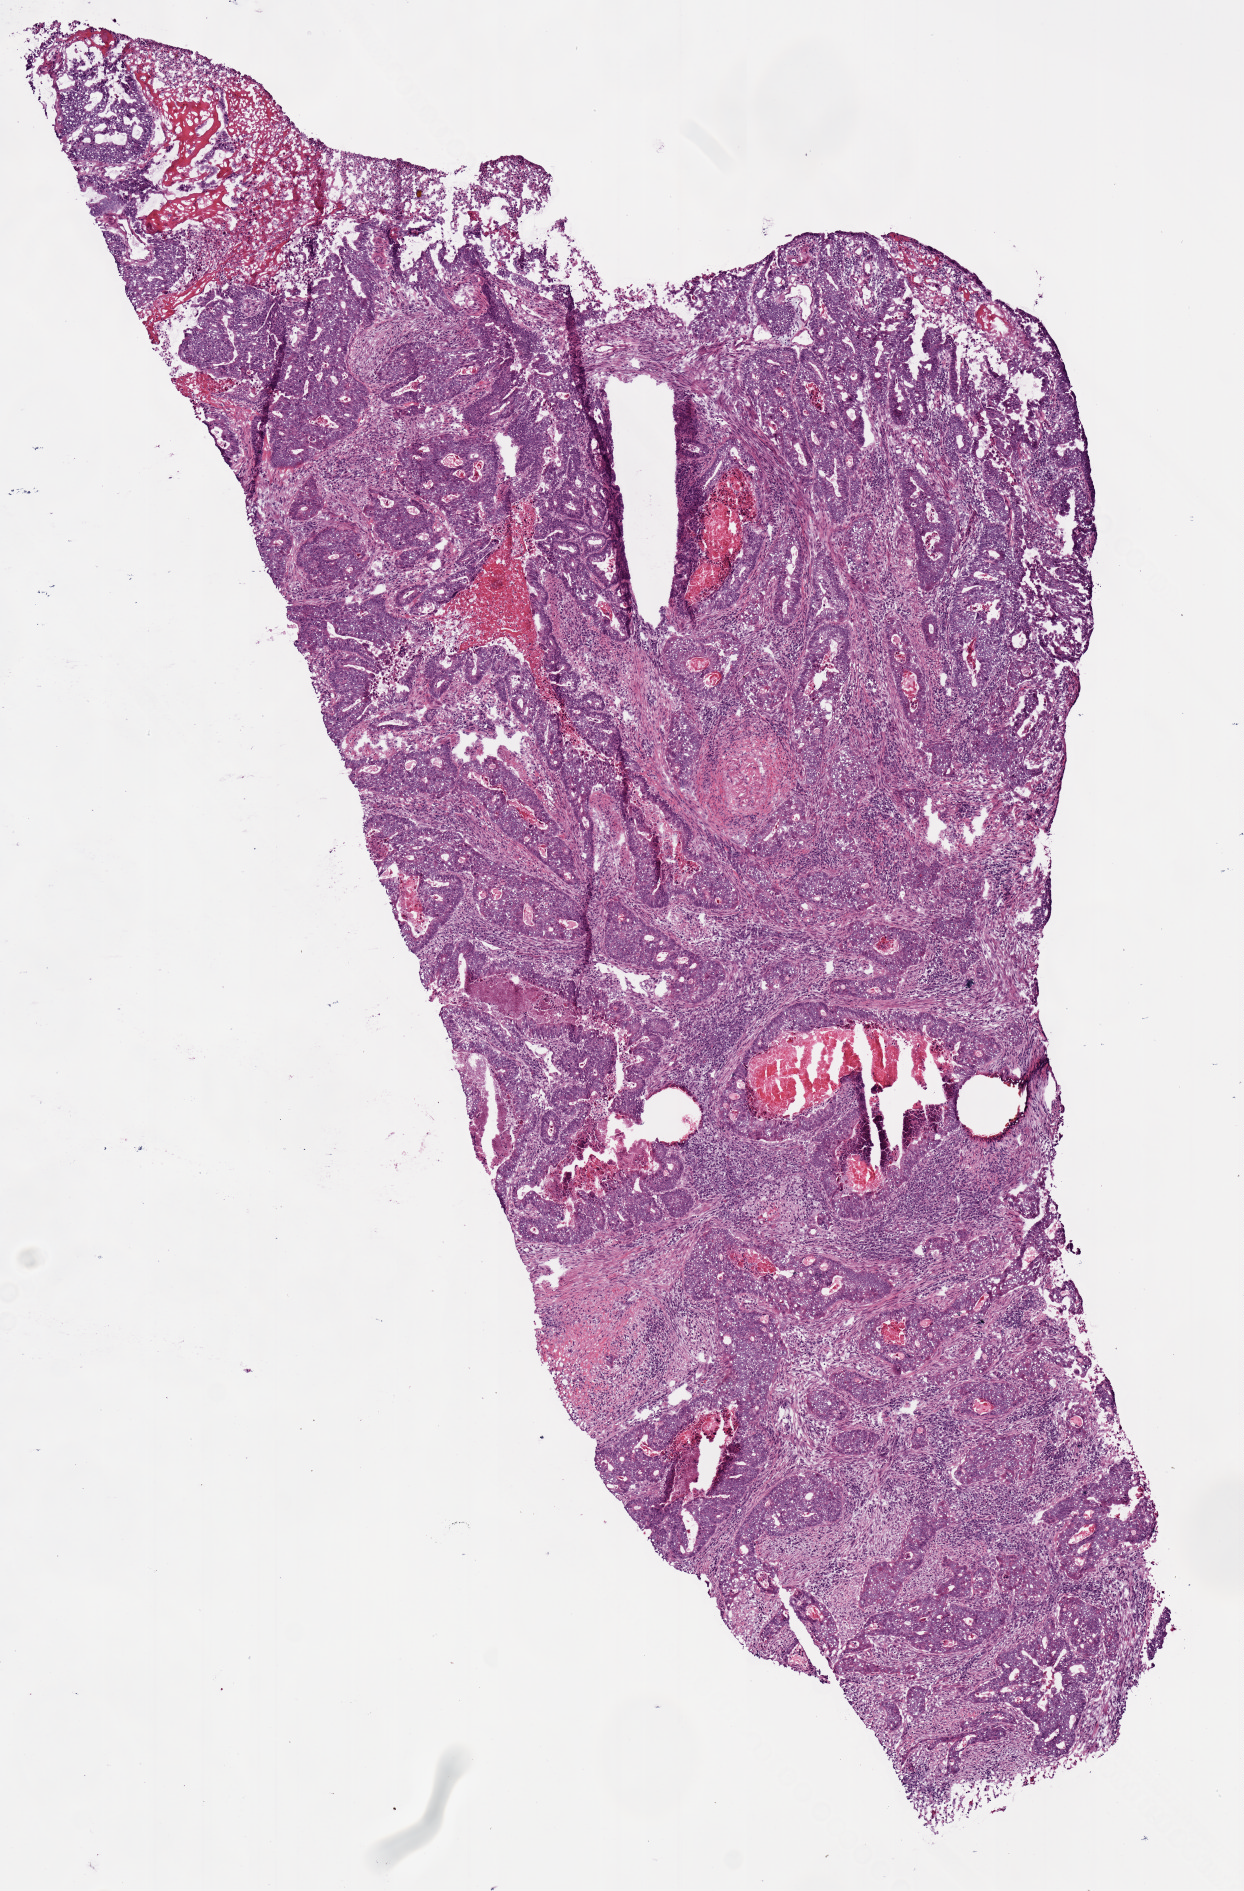
Digitized Hematoxylin and eosin (H&E) stained tissue section (whole slide), whole scanned area (about 4.9 x 7.5 mm, acquisition: 20x scan) shown as a low-resolution overview; frozen section from the bottom of the tissue portion; sample: primary tumour, colon. Female, age 49 years at initial diagnosis.
* AJCC pathologic stage: IV (7th edition)
* histologic diagnosis: Adenocarcinoma, NOS